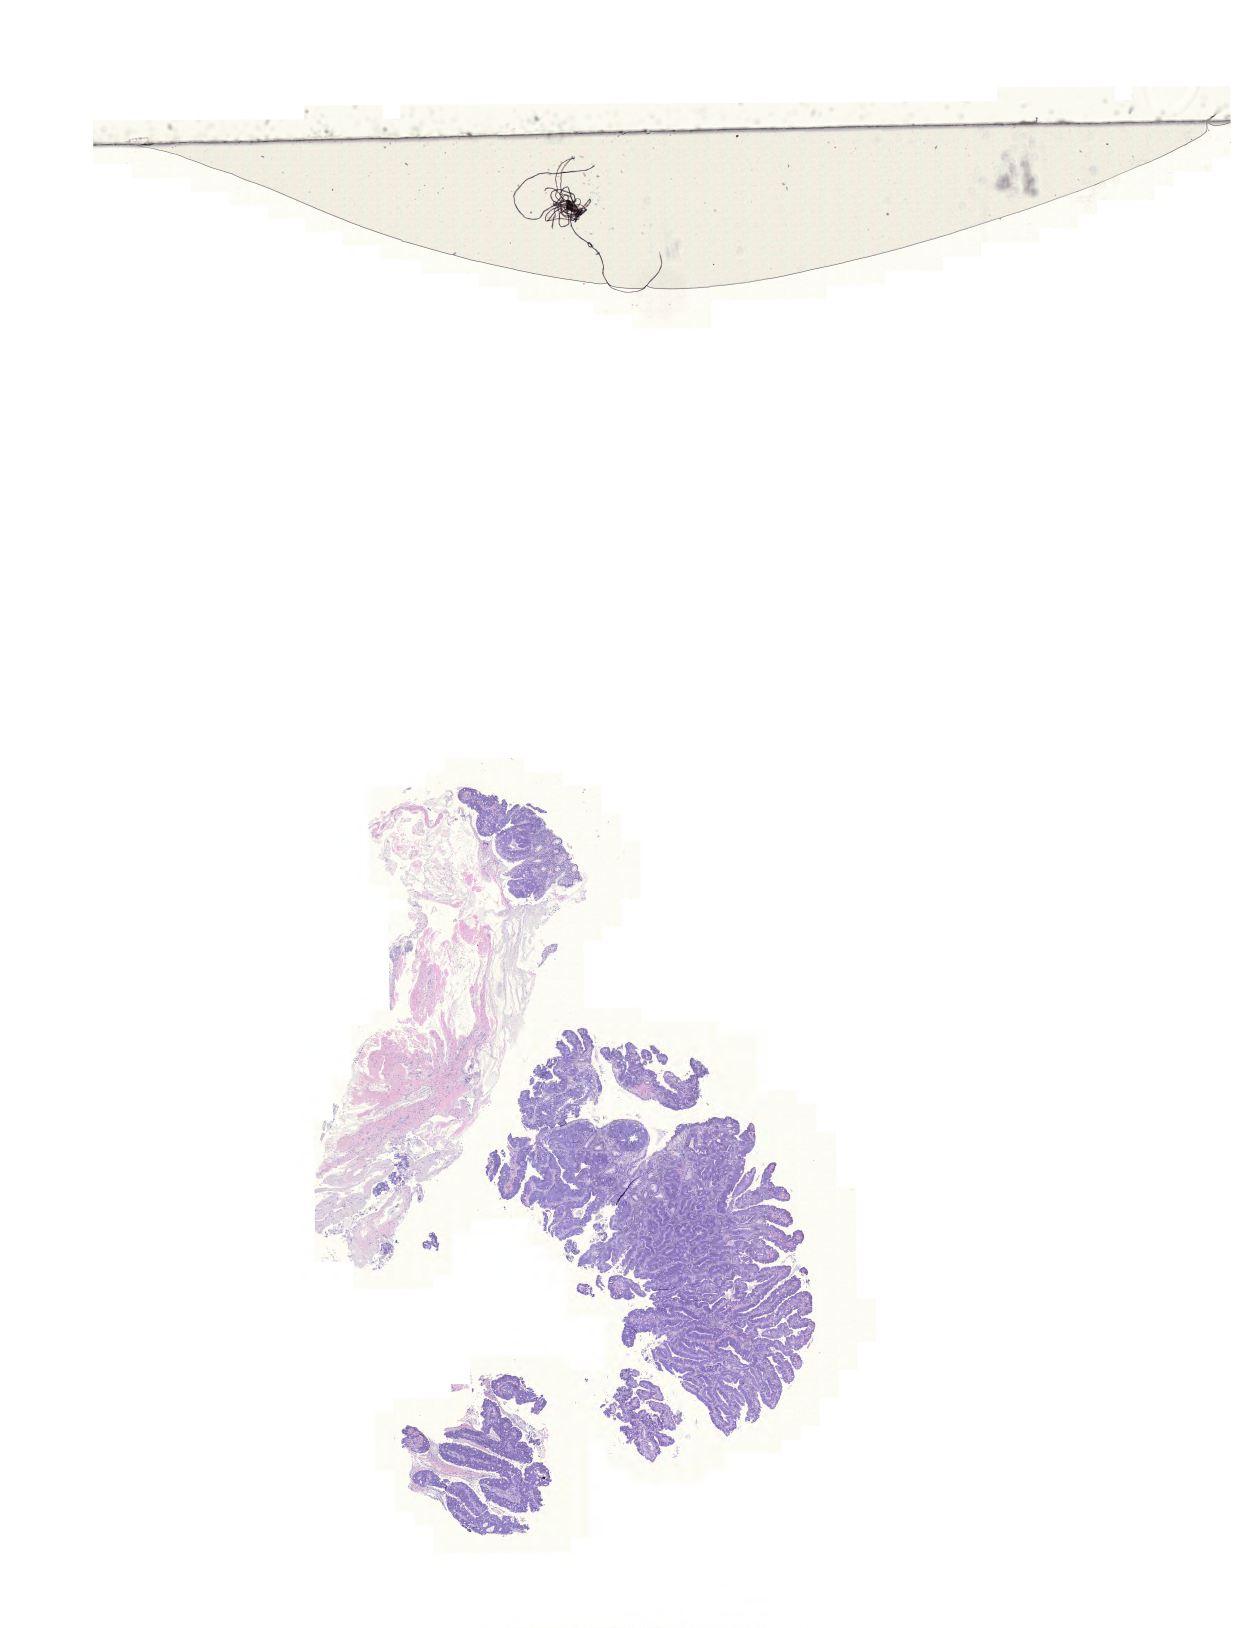
Hematoxylin and eosin (H&E) stained whole-slide image, whole scanned area (about 18.6 x 24.2 mm) shown as a low-resolution overview. FFPE section. Sample: primary tumour, rectum. Female, age 57 years at initial diagnosis.
* TNM: T1 N0 M0
* lymph nodes positive (case pathology): 0 of 17 examined
* AJCC pathologic stage: I (6th edition)
* pathologic diagnosis: Adenocarcinoma, NOS